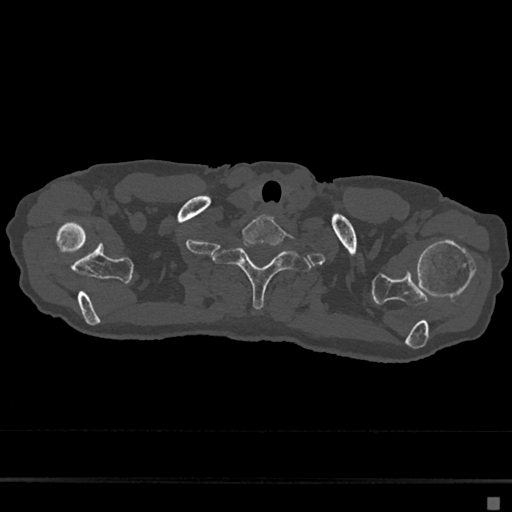
CT including the spine, one axial slice; reconstruction kernel Br40s/3; 120 kVp; bone window (W 1800 / L 400 HU); 512 × 512 image matrix, field of view 360 × 360 mm. Female patient, age 68 years. From the clinical record (not read from this slice): primary cancer: renal.
Annotated regions visible in this slice (semi-automatic segmentation, software-assisted and operator-edited):
- T1 vertebra: bounding box (x1, y1, x2, y2) in pixels: (214, 239, 312, 309)